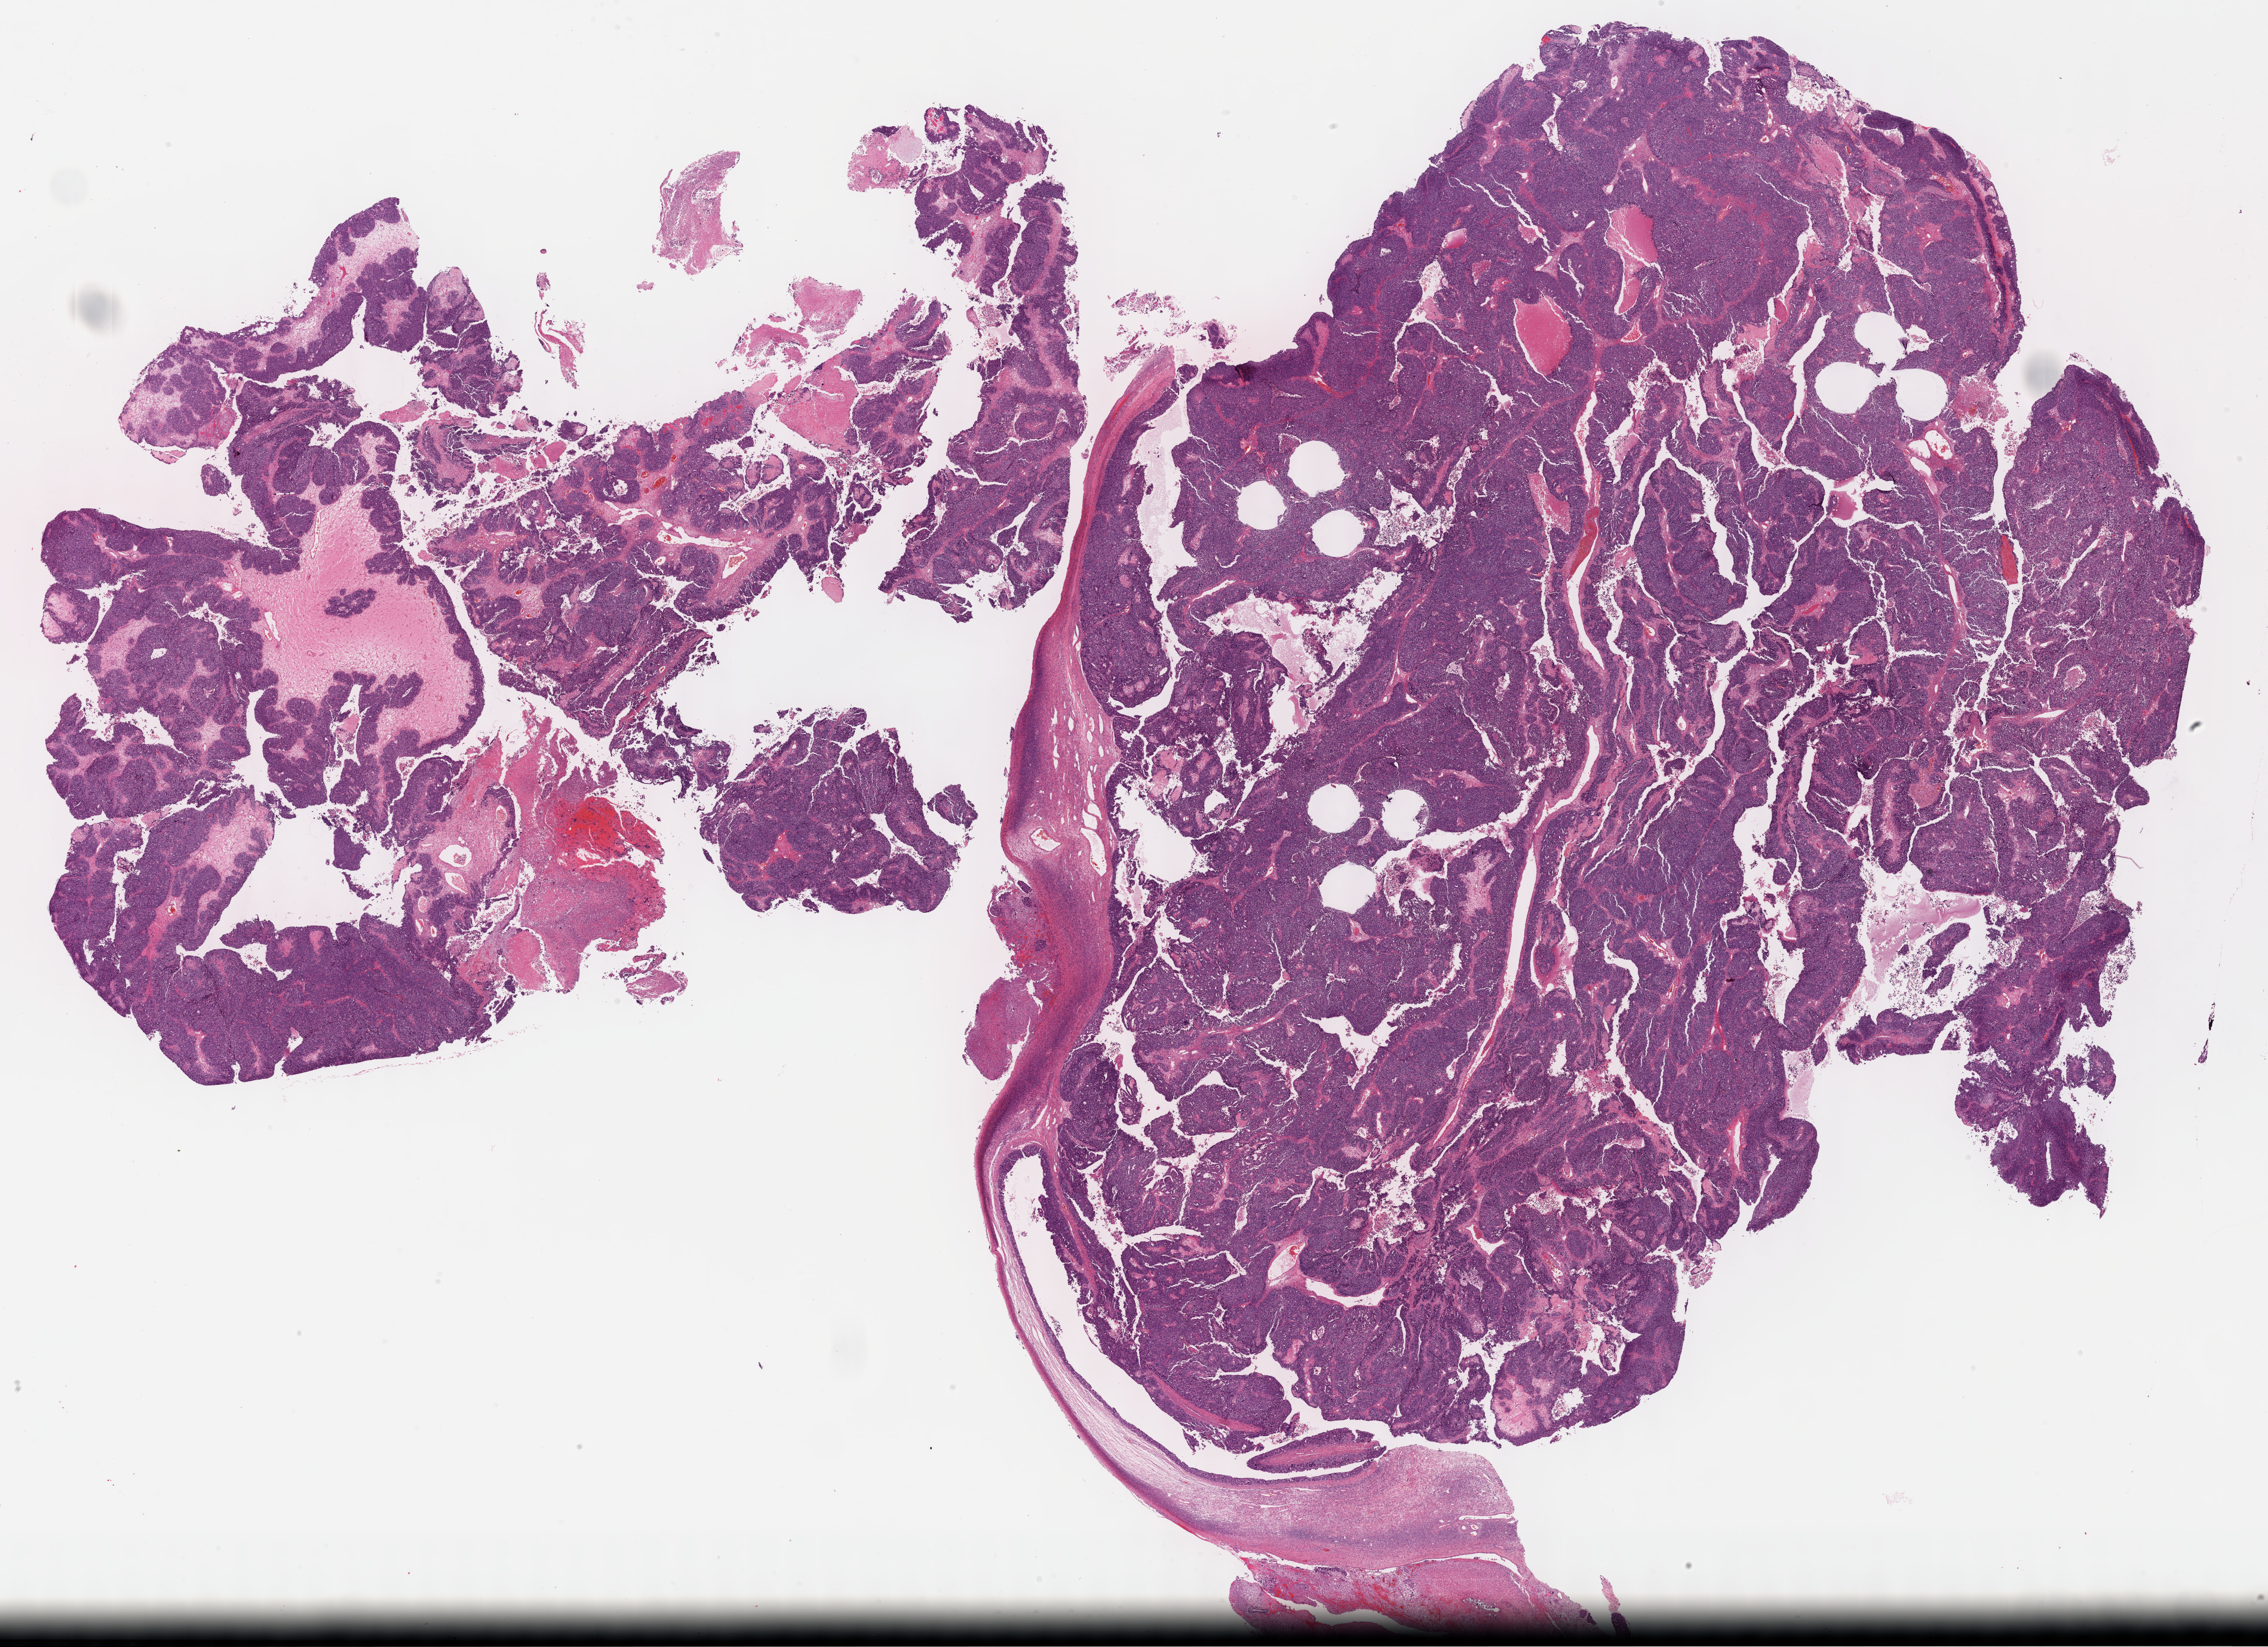
Digitized Hematoxylin and eosin (H&E) stained tissue section (whole slide), low-resolution overview of the scanned area, about 30.7 x 22.3 mm (from a 40x scan); formalin-fixed paraffin-embedded (FFPE) diagnostic section; sample: primary tumour, ovary. Female patient; age at initial diagnosis 42 years. Histologic grade: G3 (poorly differentiated).
Laterality: right. FIGO stage: IIIC. Histologic diagnosis: Serous cystadenocarcinoma, NOS.